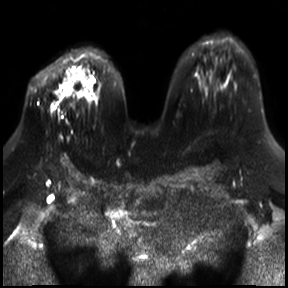
Breast MRI, one axial slice; position 19 of 30 along the scan axis; diffusion-weighted series; image 2 of 4 stored at this slice position (different b-values; order by instance number); 3 T; 4 mm slice thickness; 288 × 288 image matrix, field of view 340 × 340 mm. Female patient.
Structures marked on this image (expert manual segmentation):
- tumour on diffusion-weighted imaging: box from (x=62, y=84) to (x=72, y=96) px